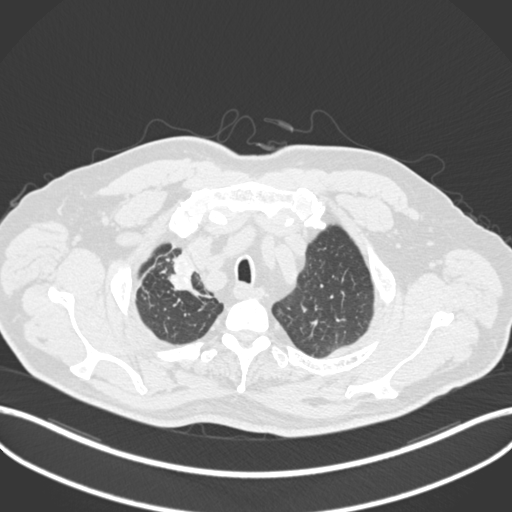
Chest CT, one axial slice; slice 175 of 255 in the series (ordered by position); reconstruction kernel B30f; 120 kVp; lung window (W 1500 / L -600 HU); 1 mm slice thickness; 512 × 512 image matrix. Patient: male, 60 years. From the clinical record (not read from this slice): clinical TNM (as recorded): T1b N1 M0.
Annotated regions visible in this slice (bounding box drawn by a radiologist):
- lung tumour (recorded histology: squamous cell carcinoma): bounding box <158,246,204,298> (left, top, right, bottom; pixels)